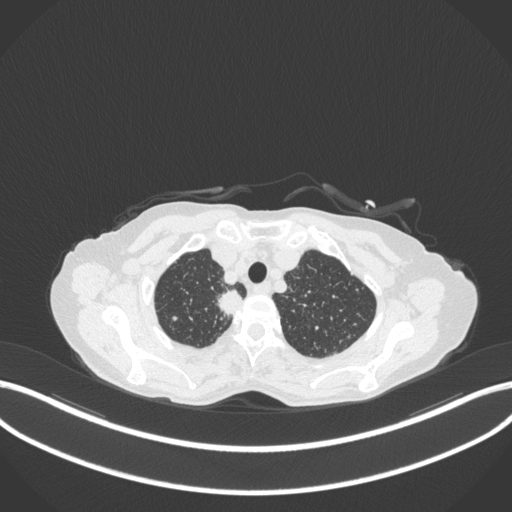
Chest CT, one axial slice. Position 322 of 363 along the scan axis. 120 kVp. Lung window (W 1500 / L -600 HU). 1 mm slice thickness. 512 × 512 image matrix. Female patient, age 75 years. Case-level facts recorded for this patient, not image findings: clinical TNM (as recorded): T1c N1 M1.
Structures marked on this image (rectangle marked by the reading radiologist):
- lung tumour (recorded histology: adenocarcinoma): bounding box [x1, y1, x2, y2] px = [214, 288, 248, 320]